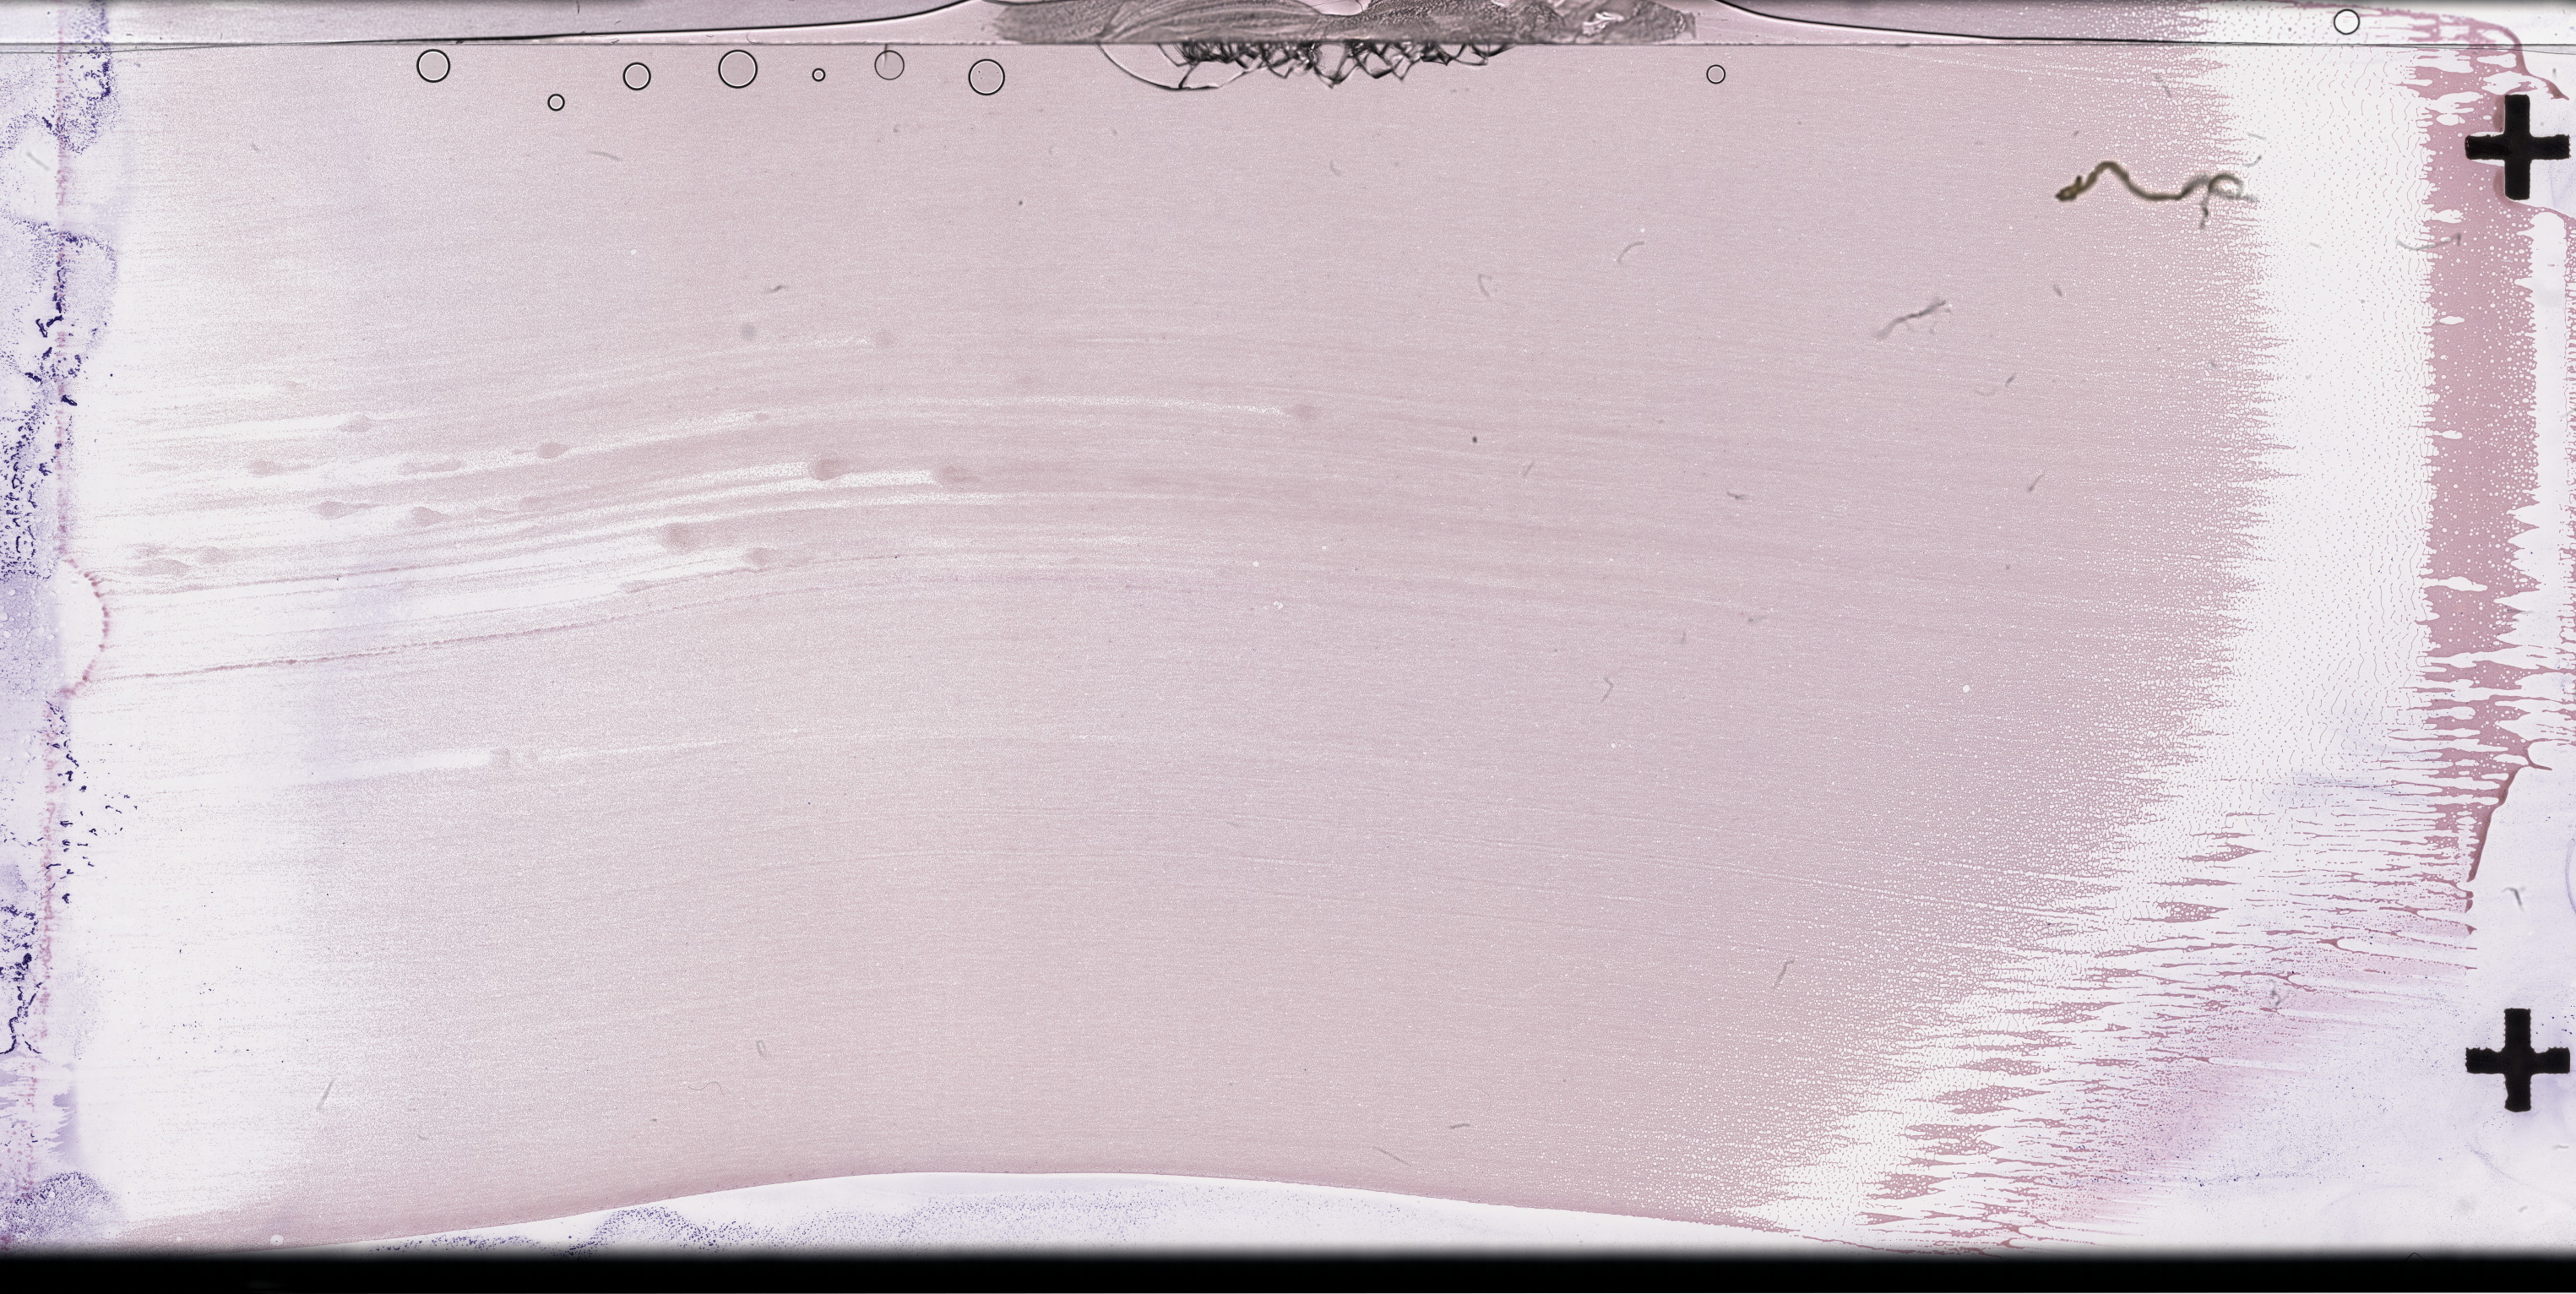
Wright-Giemsa-stained whole blood smear, whole-slide image — shown as a low-resolution overview of the whole scanned area (about 49.3 x 24.7 mm), smear from an EDTA sample, specimen time point: collected on treatment. Patient sex: female.
* from a patient with: Plasma Cell Myeloma